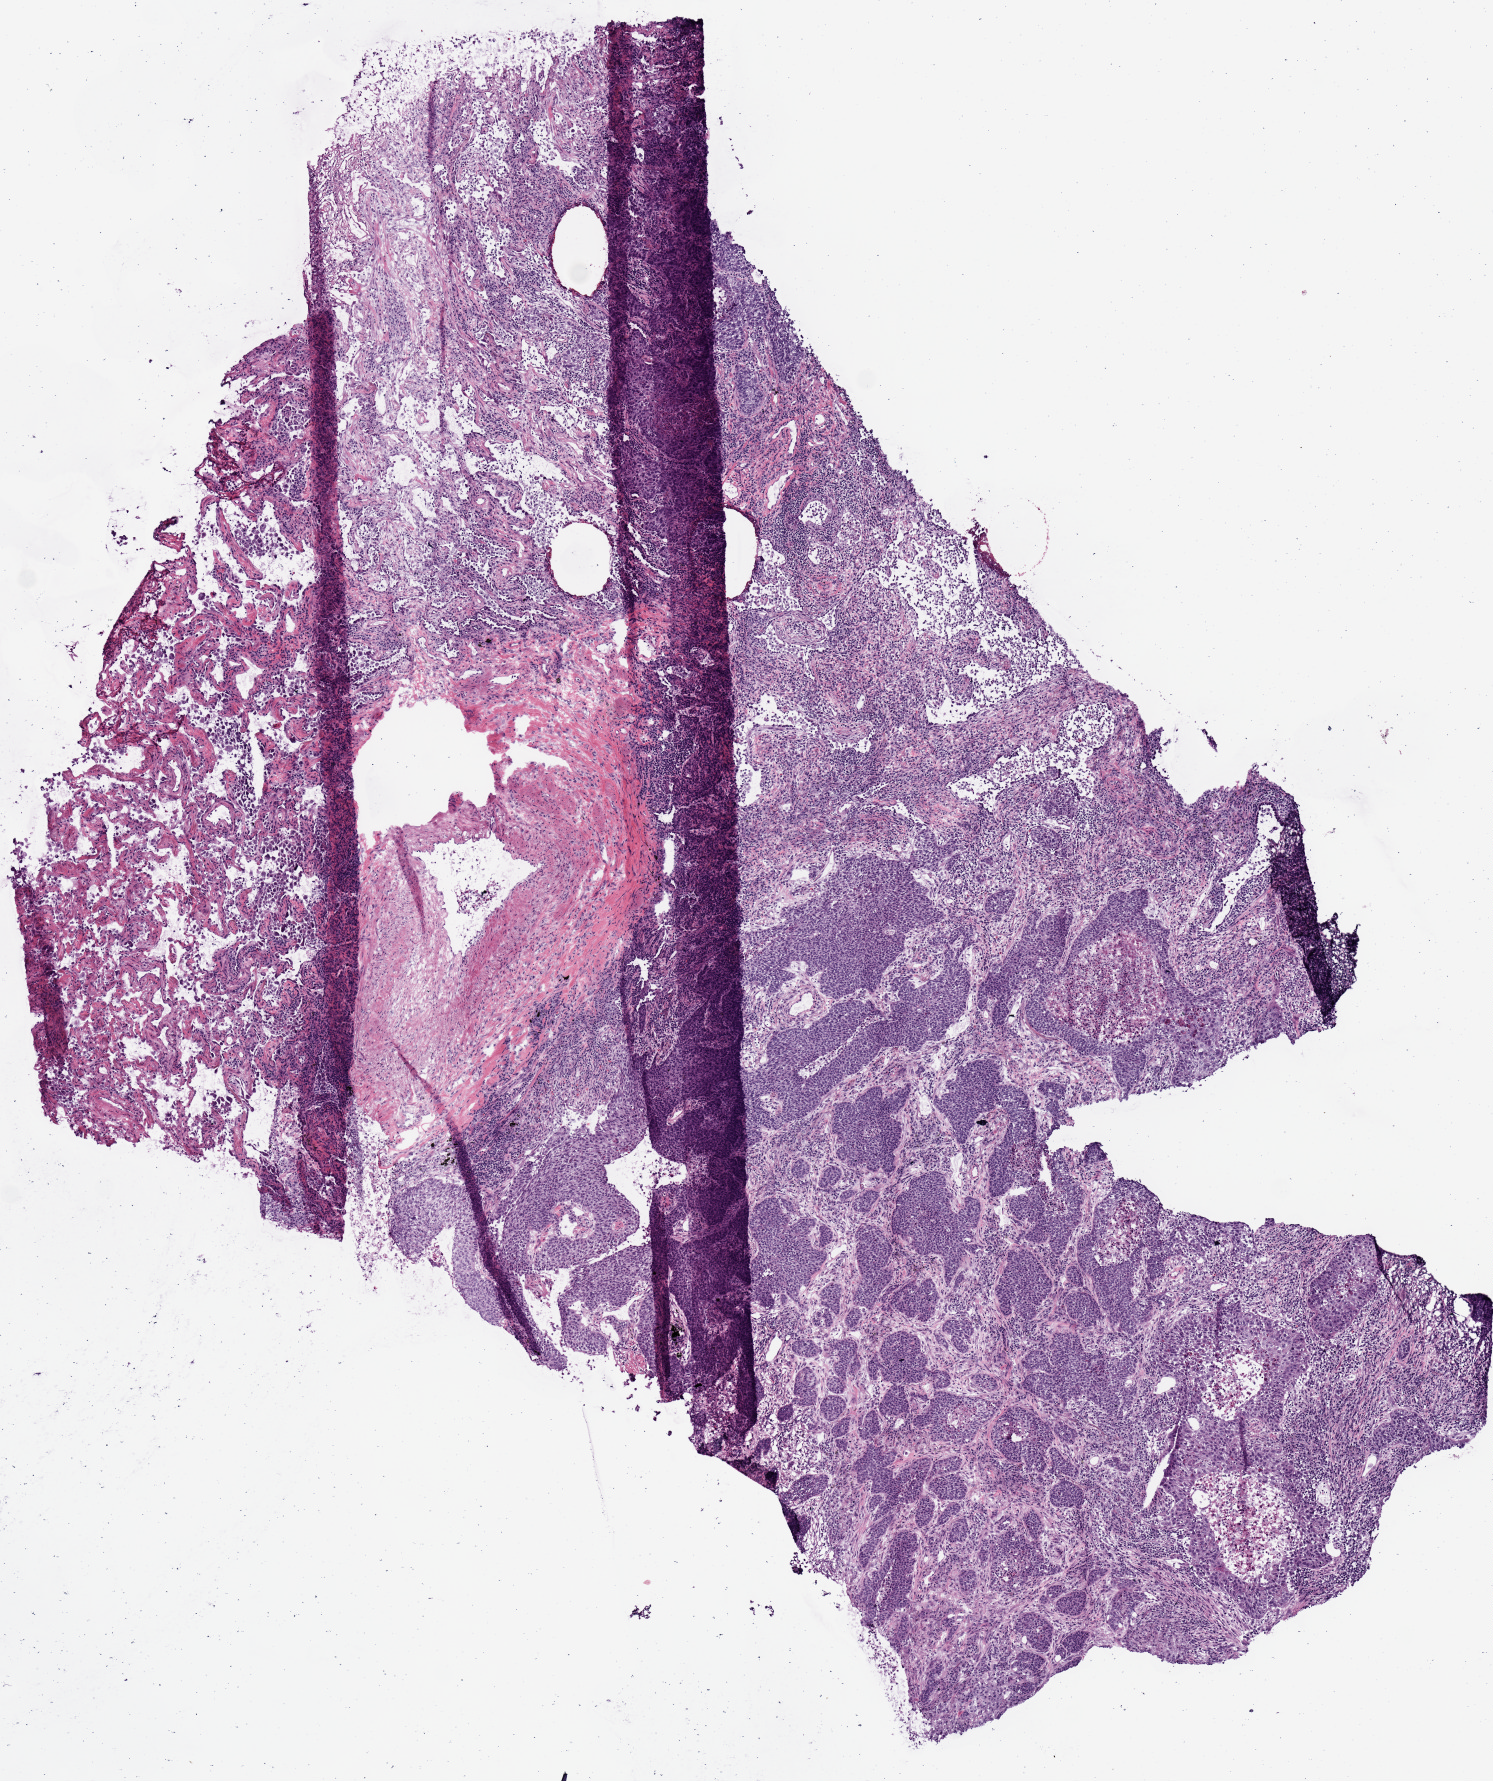
Digitized H&E tissue section (whole slide), shown as a low-resolution overview of the whole scanned area (about 5.9 x 7.0 mm, from a 20x scan); frozen section from the top of the tissue portion; lung, primary tumour sample. Patient: male, age at initial diagnosis 73 years. Pathologist review of this section (percent, as recorded): tumour cells 80%, tumour nuclei 65%, normal cells 0%, stromal cells 15%, necrosis 5%.
- pathologic diagnosis: Squamous cell carcinoma, NOS (upper lobe, lung)
- AJCC pathologic stage: IA